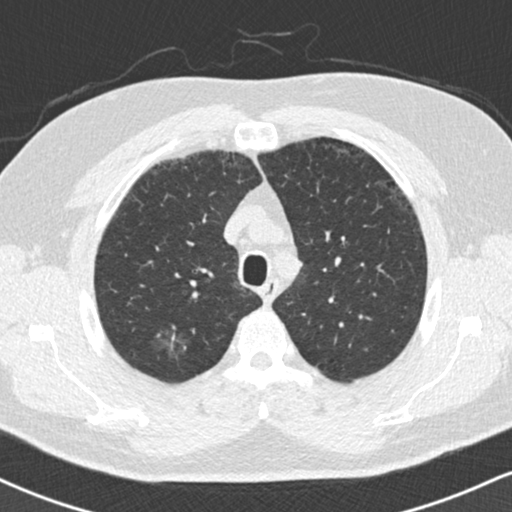
Low-dose screening chest CT, one axial slice. Slice 130 of 169 in the series (ordered by position). Reconstruction kernel B30f. Lung window (W 1500 / L -600 HU). 2 mm slice thickness. 512 × 512 image matrix, field of view 320 × 320 mm.
Annotated regions visible in this slice (expert manual segmentation):
- lesion 1 (tumor, upper lobe of right lung): box from (x=153, y=330) to (x=189, y=359) px